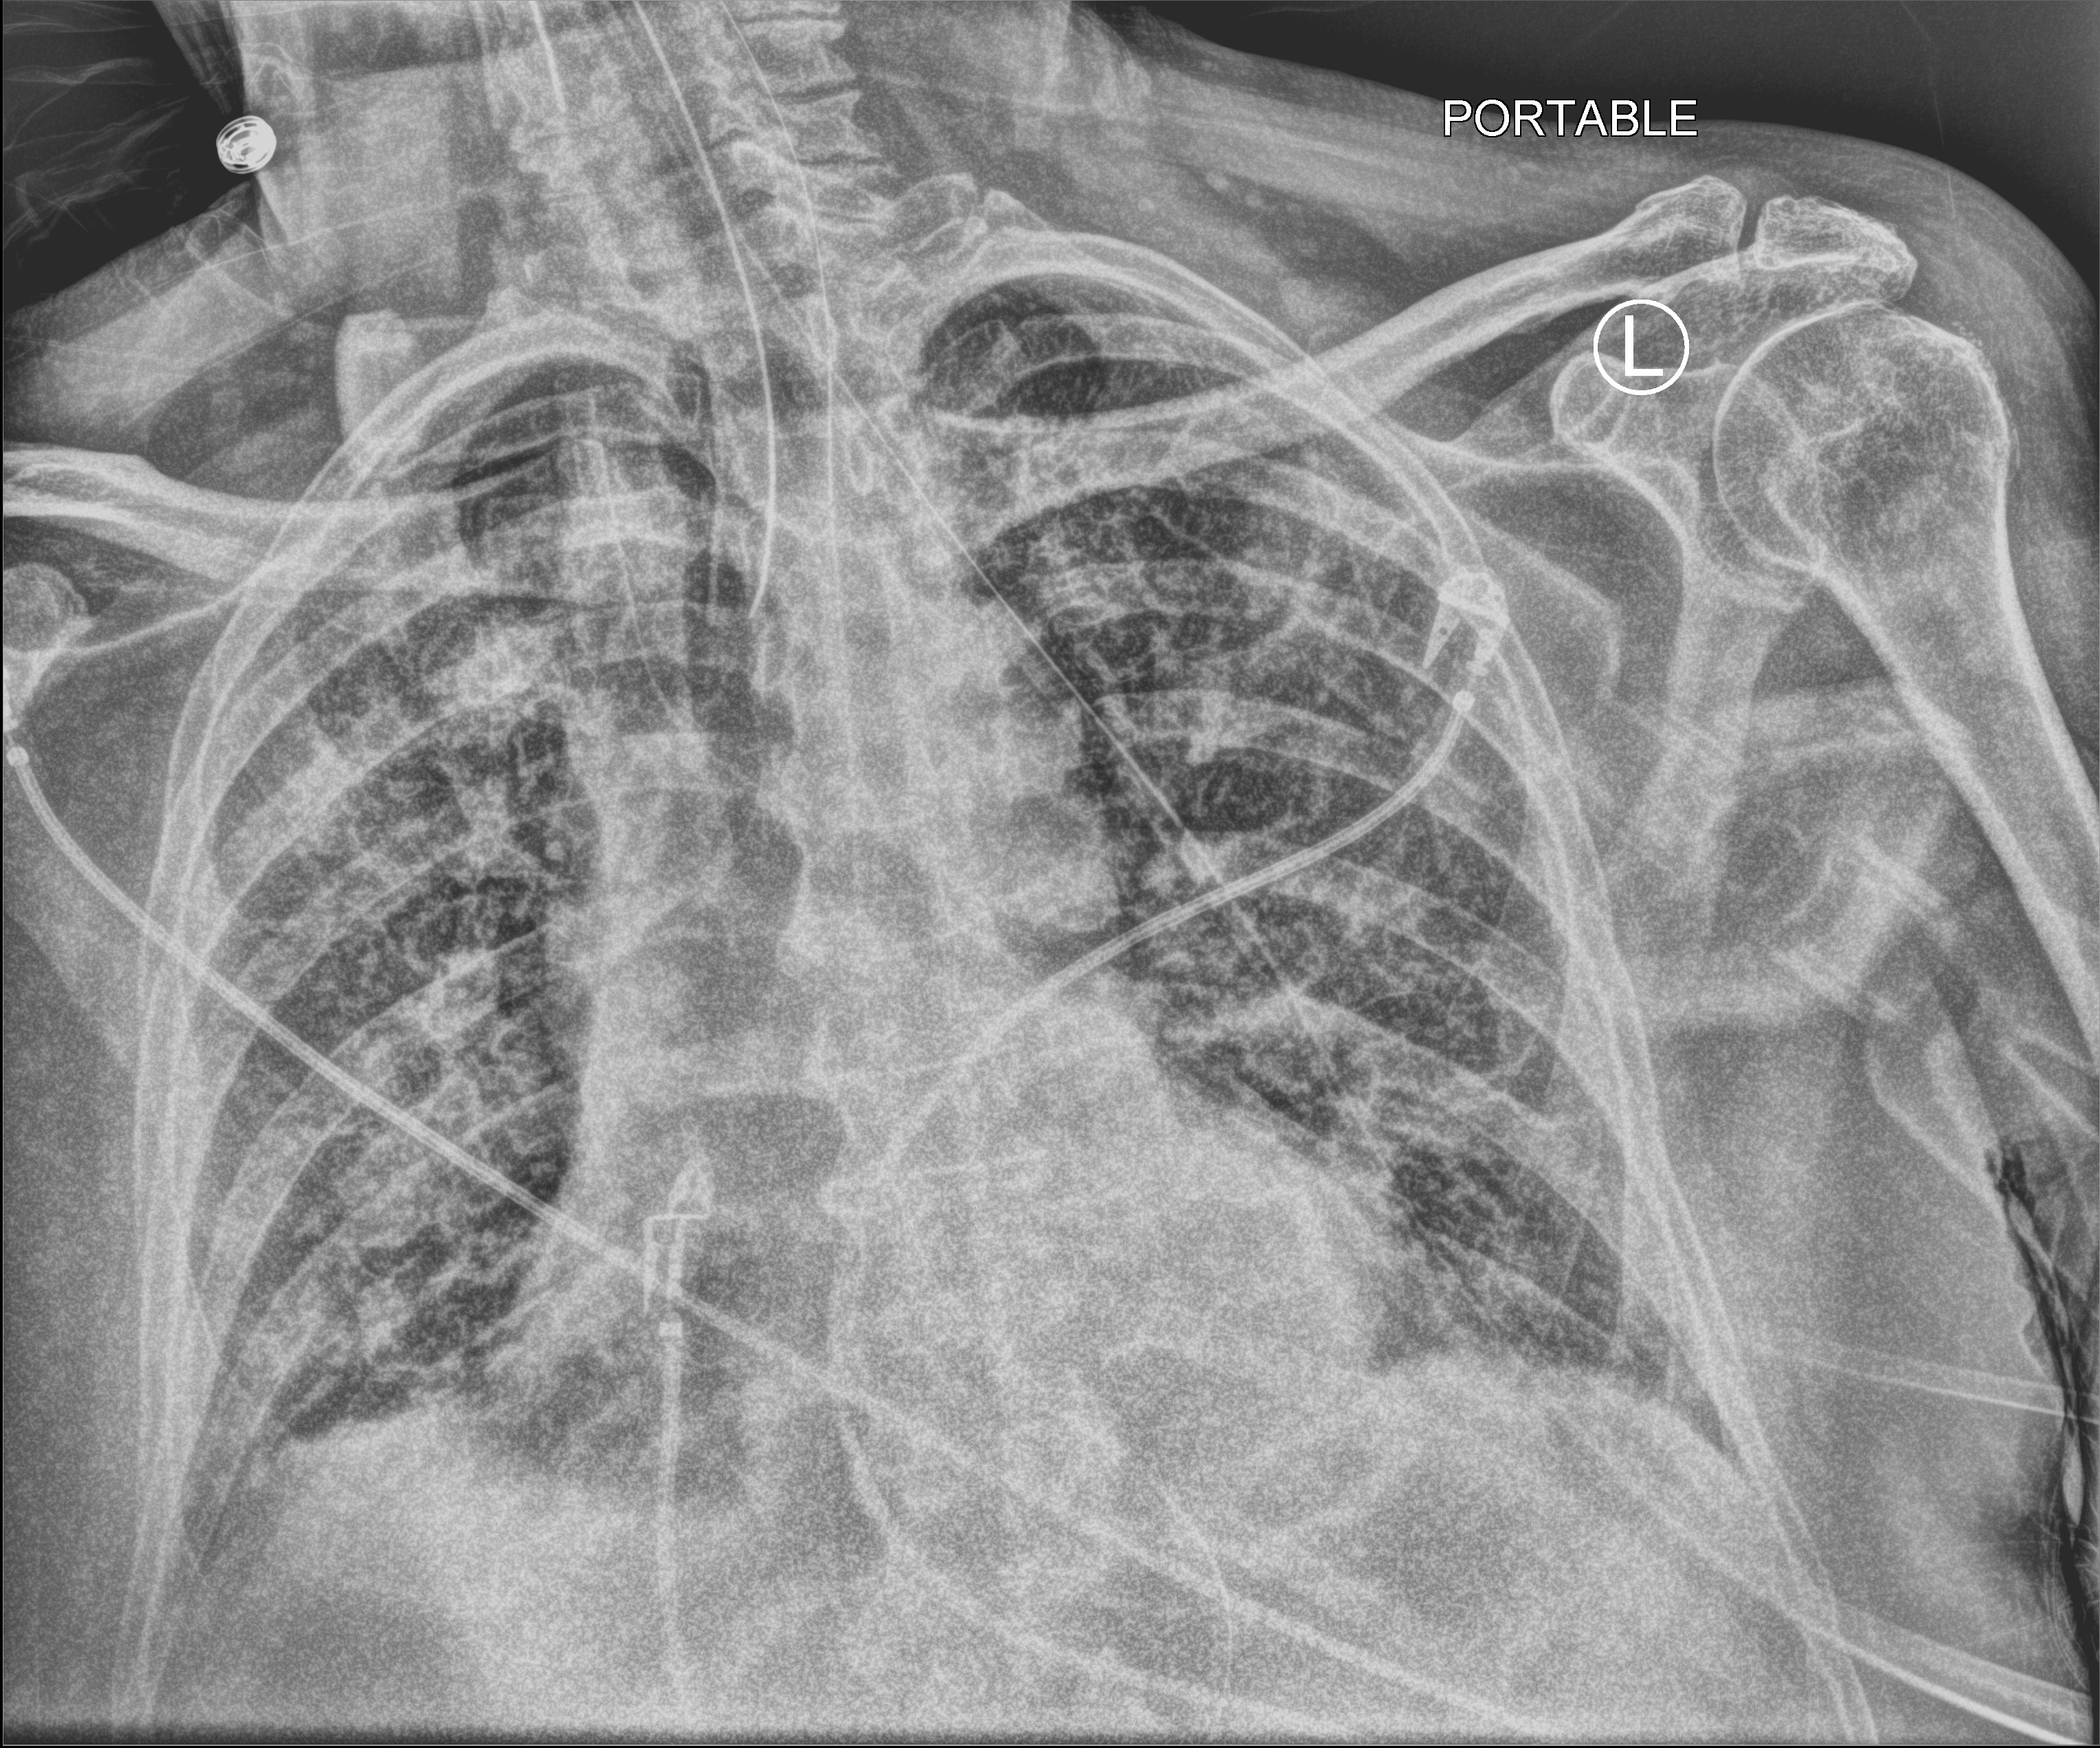
Portable chest radiograph; anteroposterior (AP) projection. Male patient hospitalised with COVID-19, age 75–90 years.
Admission-level facts for this patient (not findings on this image; timing relative to this image not recorded):
- mechanically ventilated during this hospital stay: yes